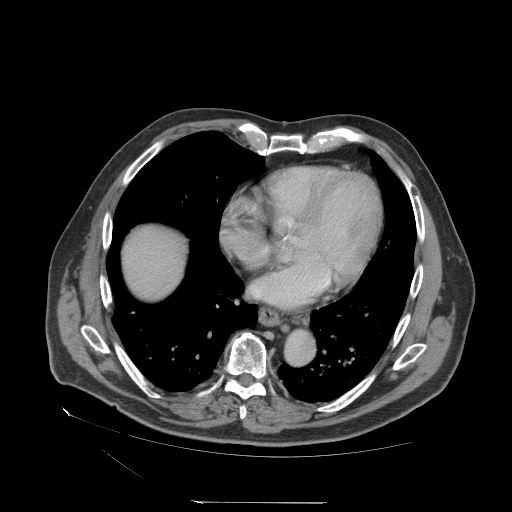
Contrast-enhanced abdominal CT (liver protocol), one axial slice; 140 kVp; soft-tissue window (W 400 / L 40 HU); 512 × 512 image matrix. From the clinical record (not read from this slice): diagnosis: hepatocellular carcinoma (patient treated with transarterial chemoembolisation; whether this scan precedes or follows treatment is not stated here); TNM stage (as recorded): Stage-I; Child-Pugh class: A; tumour differentiation: well differentiated.
Structures marked on this image (semi-automatically segmented with operator editing):
- liver parenchyma outside the tumour (the mass and vessels are separate outlines, so this box may not span the whole liver): bounding box [x1, y1, x2, y2] px = [122, 226, 184, 298]